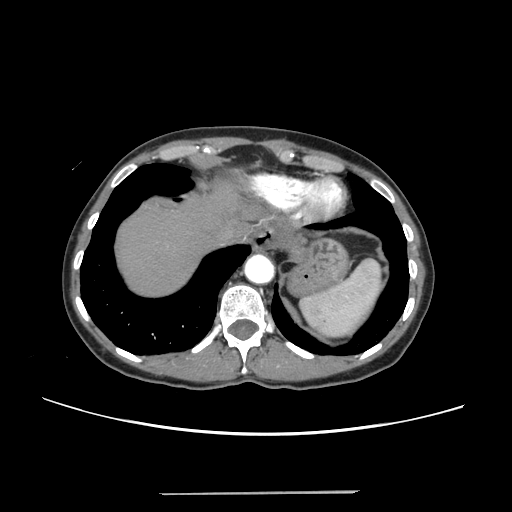
Contrast-enhanced abdominal CT, one axial slice. Slice 214 of 240 in the series (ordered by position). Intravenous contrast given. Soft-tissue window (W 400 / L 40 HU). 1.25 mm slice thickness. 512 × 512 image matrix, field of view 371 × 371 mm. Female patient, age 60 years. From the clinical record (not read from this slice): diagnosis: colorectal cancer liver metastases, imaged before liver resection; multiple liver metastases: no; largest metastasis: 1.5 cm; chemotherapy before resection: yes.
Structures marked on this image (expert manual segmentation):
- liver: box from (x=116, y=185) to (x=243, y=297) px
- planned liver remnant (the part of the liver to remain after resection): (x=116, y=184)–(x=243, y=296)